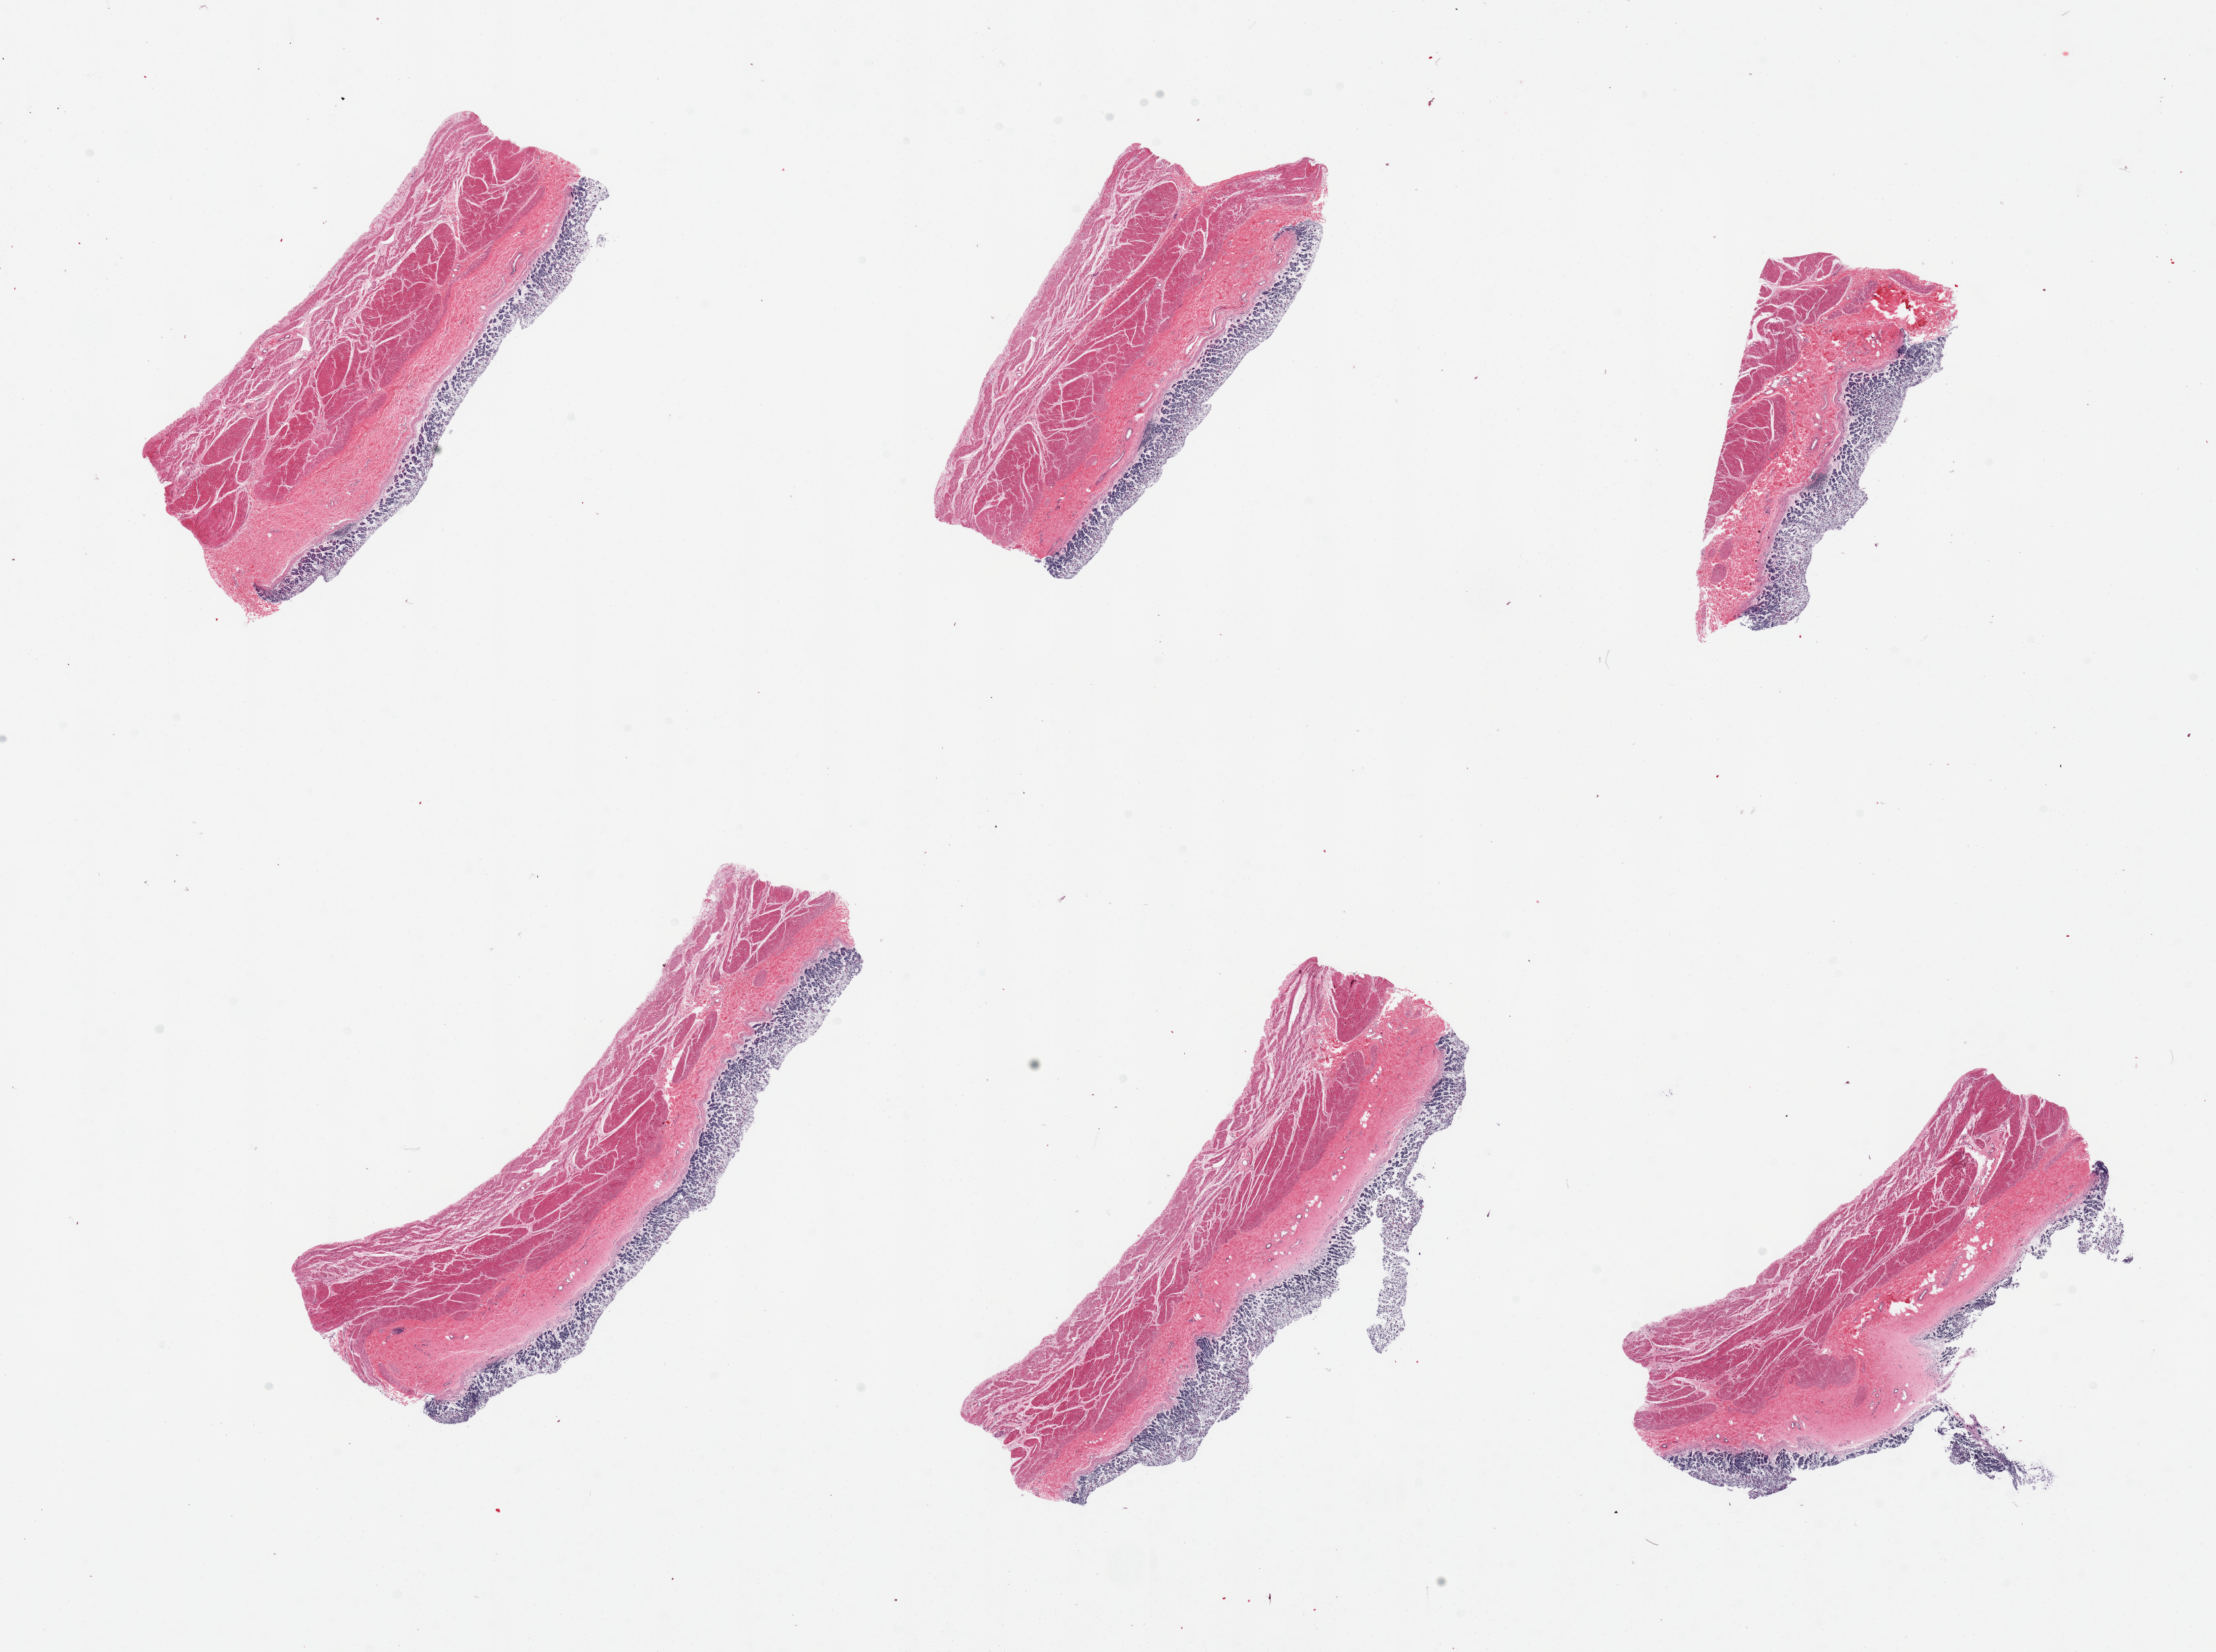
Digitized H&E-stained section — shown as a low-resolution overview of the whole scanned area (about 26.6 x 19.8 mm, acquisition: 20x scan), PAXgene-fixed paraffin-embedded (PFPE) section, target tissue: stomach, donor tissue sample. Female donor.
Reviewer comment on this tissue sample: 6 pieces, mucosa autolyzed, muscularis less so.